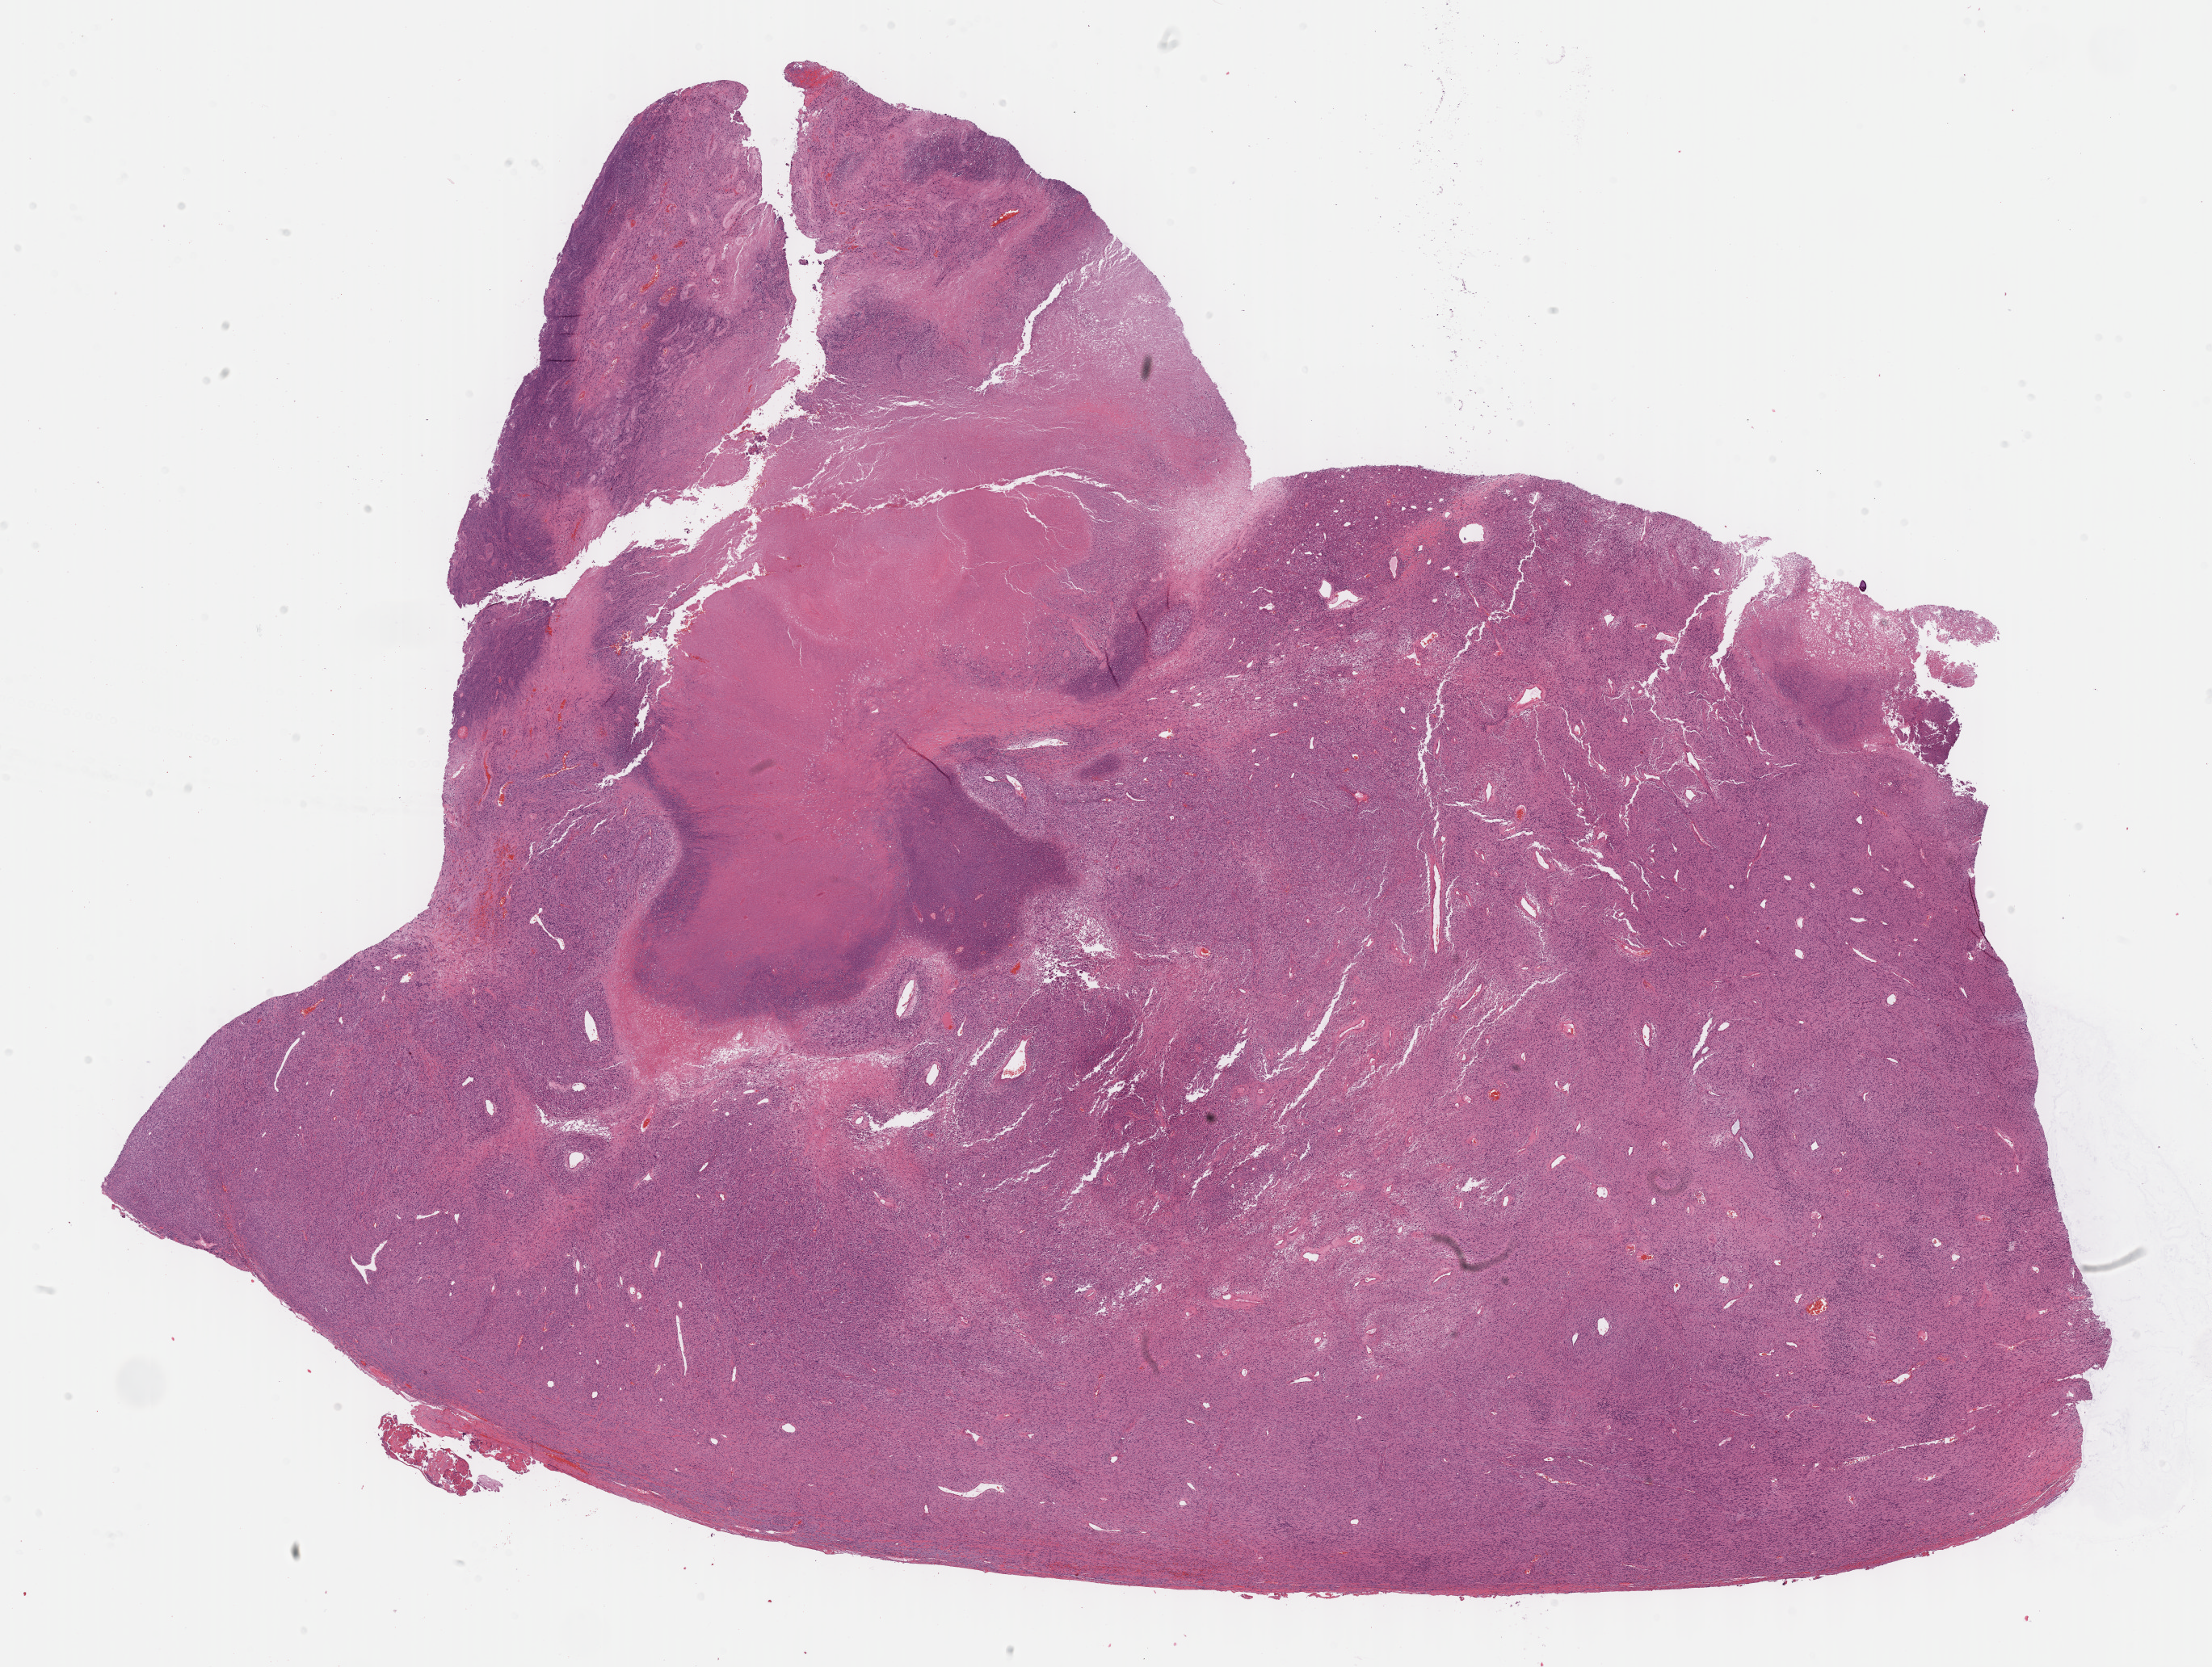
Digitized Hematoxylin and eosin (H&E) stained tissue section (whole slide) — a low-resolution overview of the entire scanned area, about 22.1 x 16.7 mm; FFPE section; connective, subcutaneous and other soft tissues, primary tumour sample. Male patient; age at initial diagnosis 52 years.
- pathologic diagnosis: Malignant peripheral nerve sheath tumor (connective, subcutaneous and other soft tissues of head, face, and neck)